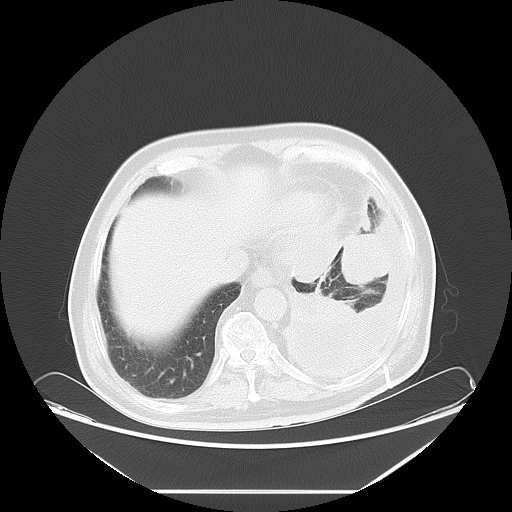
Chest CT, one axial slice; position 17 of 63 along the scan axis; reconstruction kernel LUNG; 120 kVp; lung window (W 1500 / L -600 HU); 5 mm slice thickness; 512 × 512 image matrix. Male patient, age 67 years. Case-level facts recorded for this patient, not image findings: clinical TNM (as recorded): T1b N1 M1a.
Annotated regions visible in this slice (bounding box drawn by a radiologist):
- lung tumour (recorded histology: small cell carcinoma): bounding box <336,228,391,286> (left, top, right, bottom; pixels)